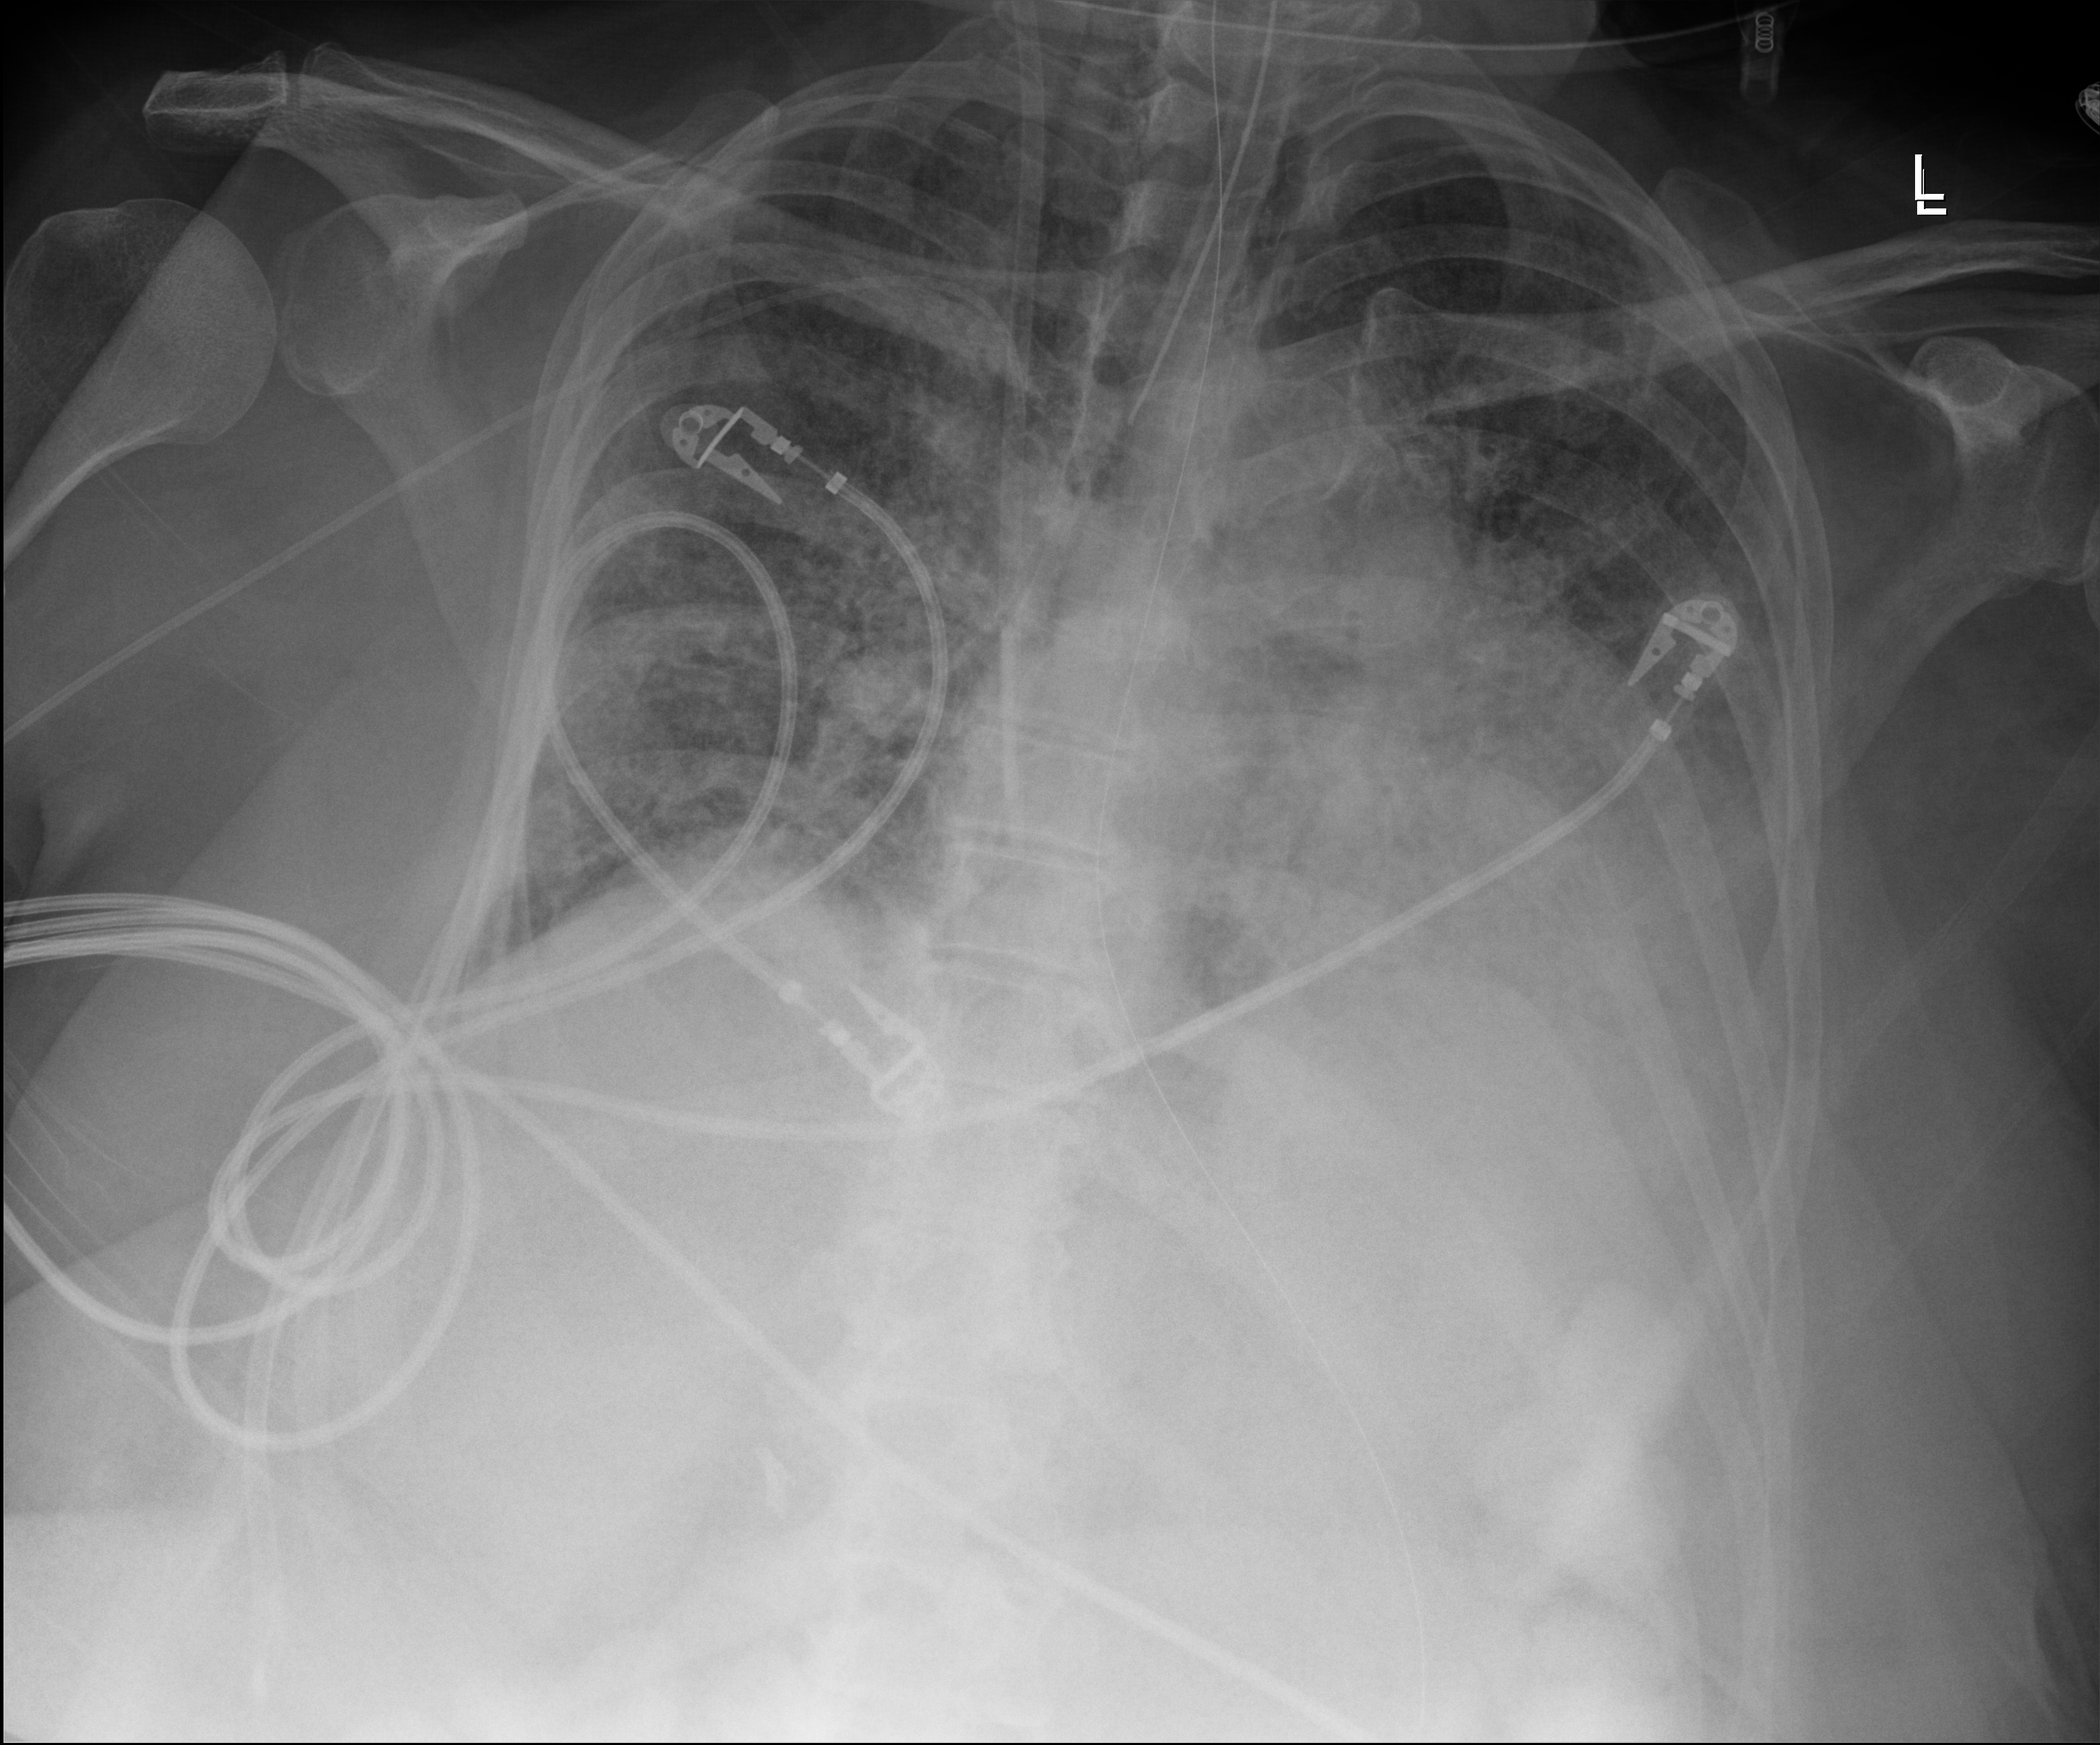
Chest radiograph. Female patient hospitalised with COVID-19, age 60–74 years.
Hospital-stay facts (about this admission, not read from this image; timing relative to this image not recorded): chronic kidney disease (admission record): no.